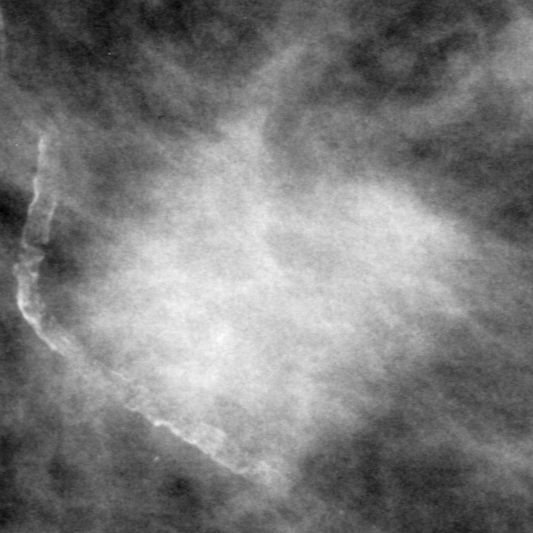
Crop from a digitized film mammogram around one marked abnormality, left breast, CC view, BI-RADS breast density category 2 (scale 1–4).
Finding: mass, shape oval, margins ill defined; BI-RADS assessment category 3; subtlety rating 4 on a 1 (subtle) to 5 (obvious) scale; pathology result (as recorded, not read from the image): malignant.